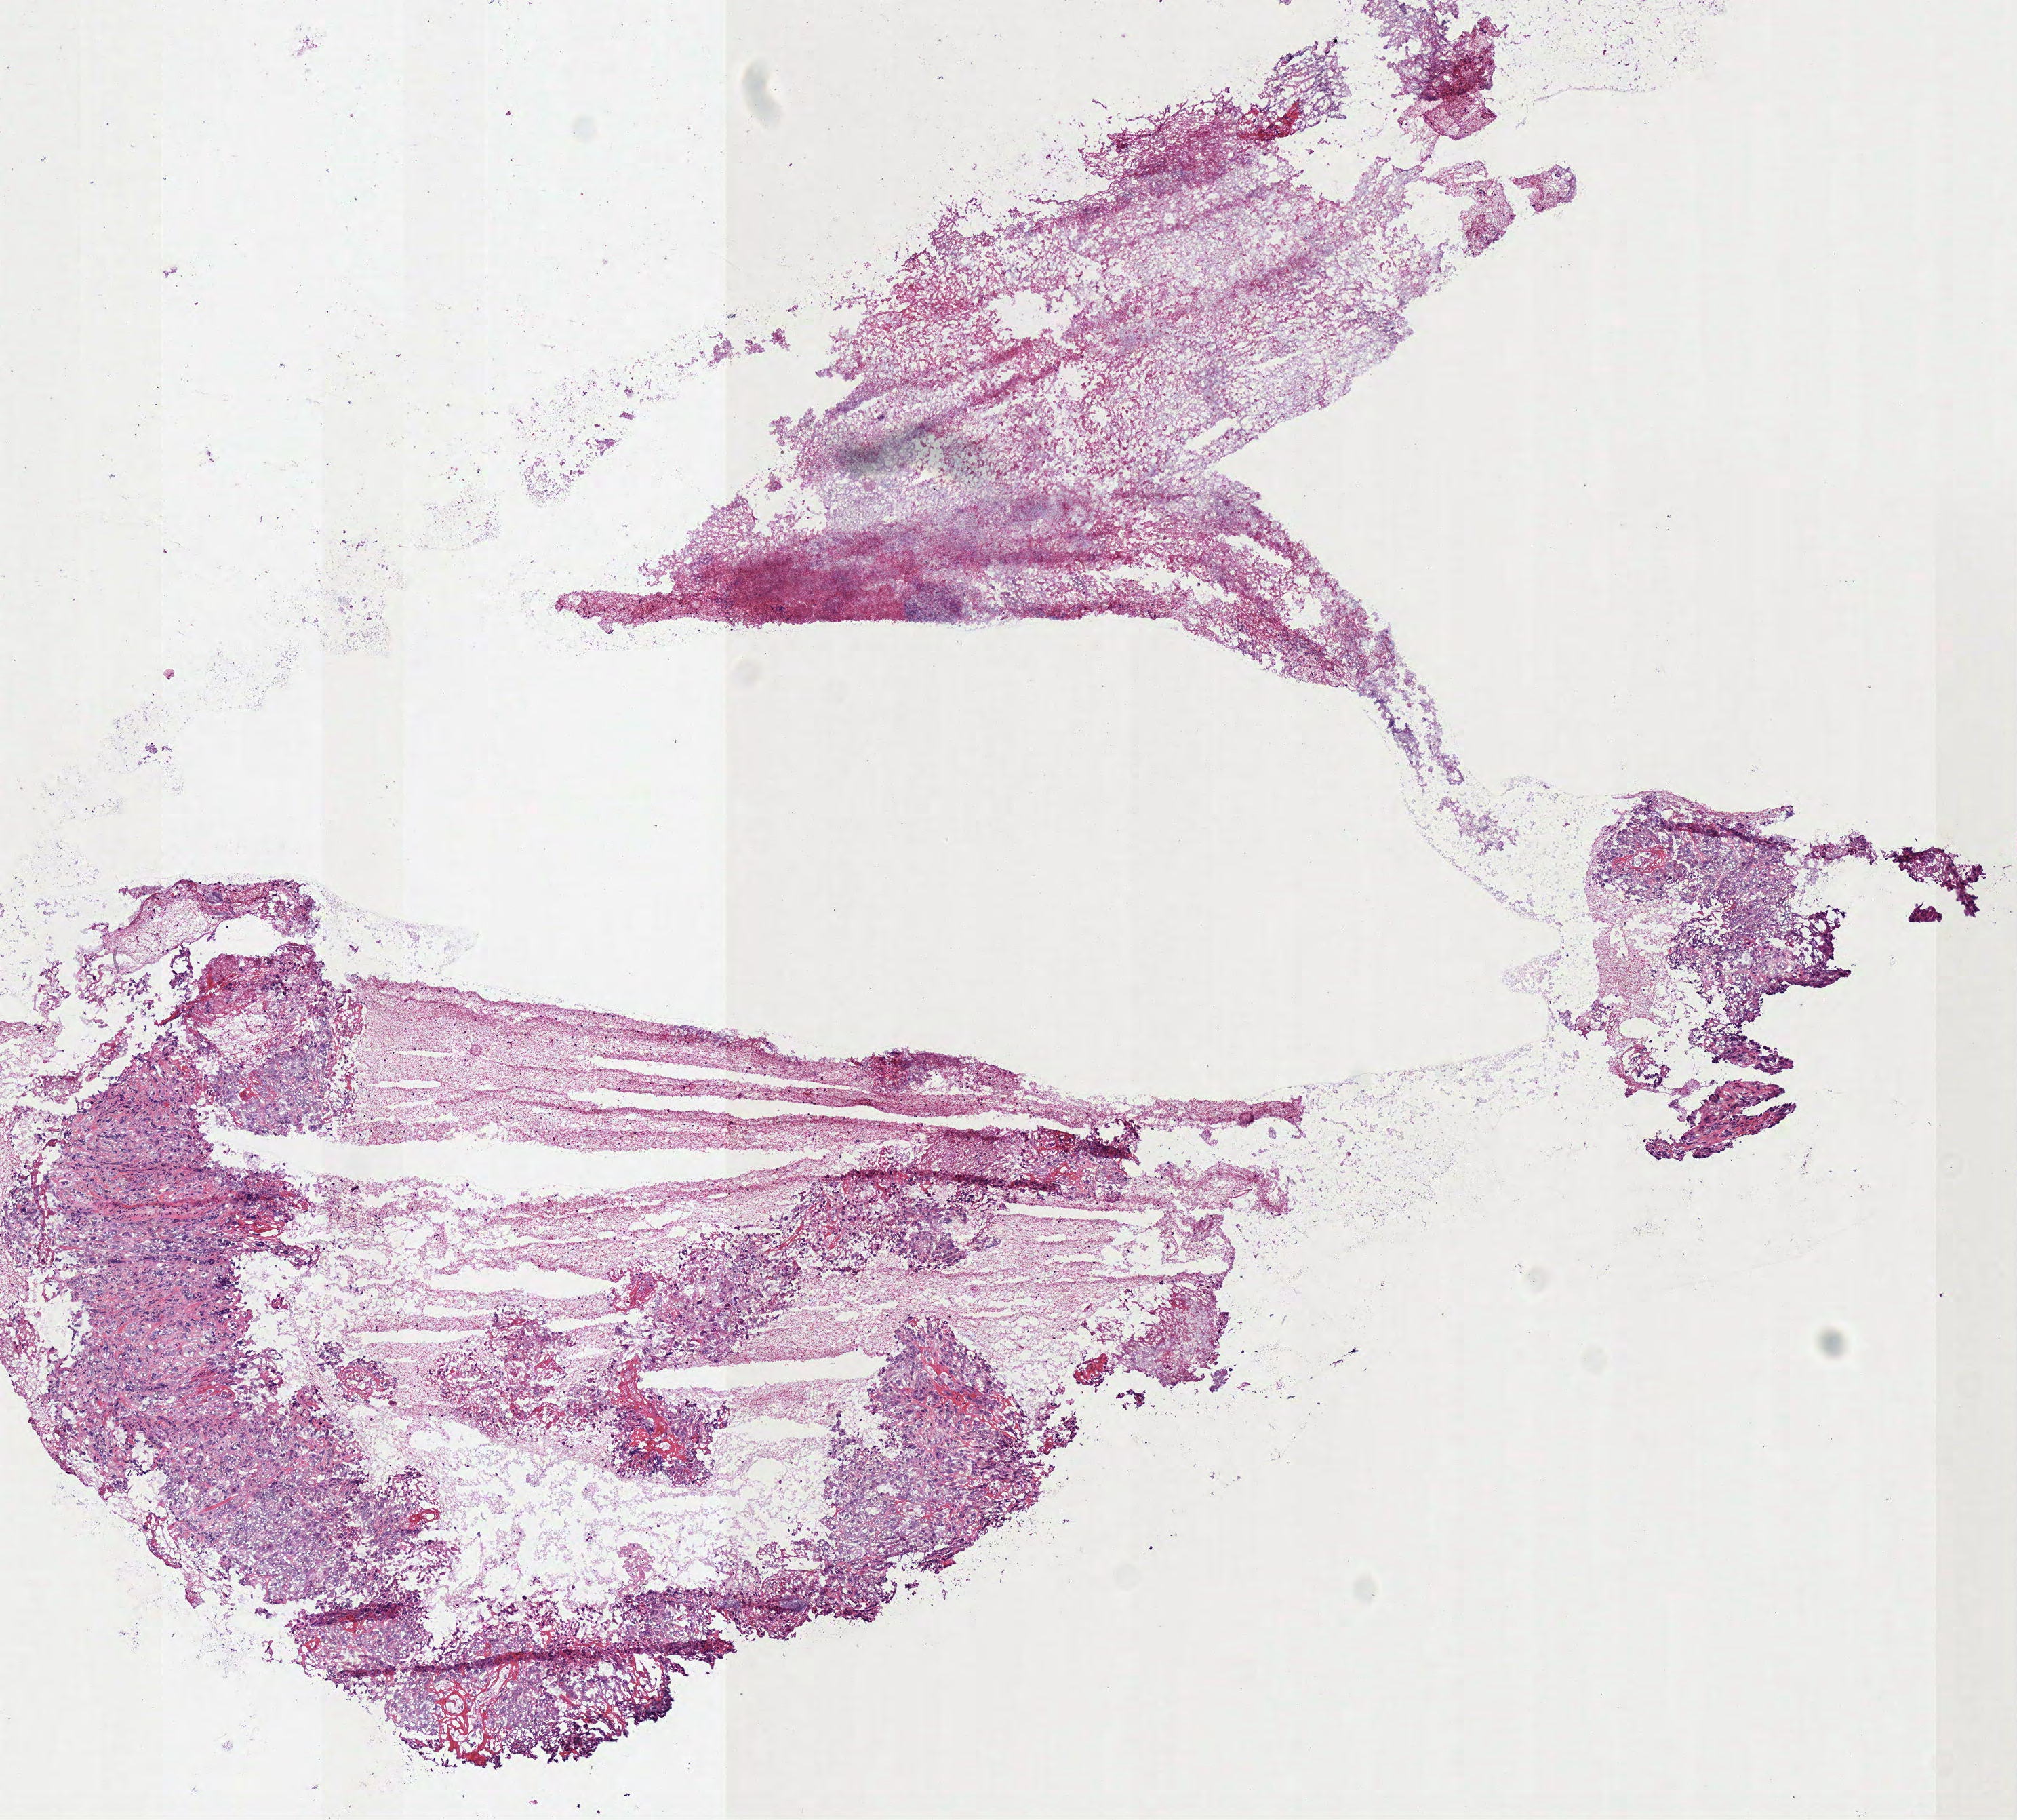
Whole-slide histology image, H&E-stained — whole scanned area (about 5.9 x 5.3 mm, acquisition: 40x scan) shown as a low-resolution overview; frozen section from the top of the tissue portion; head and neck, primary tumour sample. Patient: male, age at initial diagnosis 53 years. Histologic grade: G2 (moderately differentiated). Pathologist review of this section (percent, as recorded): tumour cells 40%, tumour nuclei 90%, normal cells 0%, stromal cells 59%, necrosis 1%.
Diagnosis: Squamous cell carcinoma, NOS.